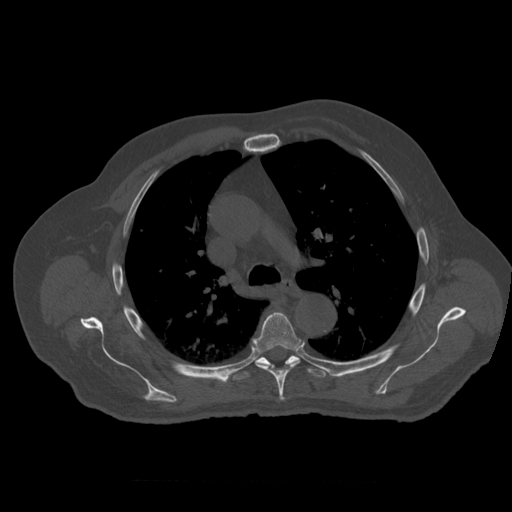
CT including the spine, one axial slice; reconstruction kernel STANDARD; bone window (W 1800 / L 400 HU); 512 × 512 image matrix. Patient age 73 years. Case-level facts recorded for this patient, not image findings: primary cancer: prostate.
Outlined on this slice (semi-automatic segmentation, software-assisted and operator-edited):
- T5 vertebra: bounding box <253,313,301,402> (left, top, right, bottom; pixels)
- T6 vertebra: <233,356,327,381>